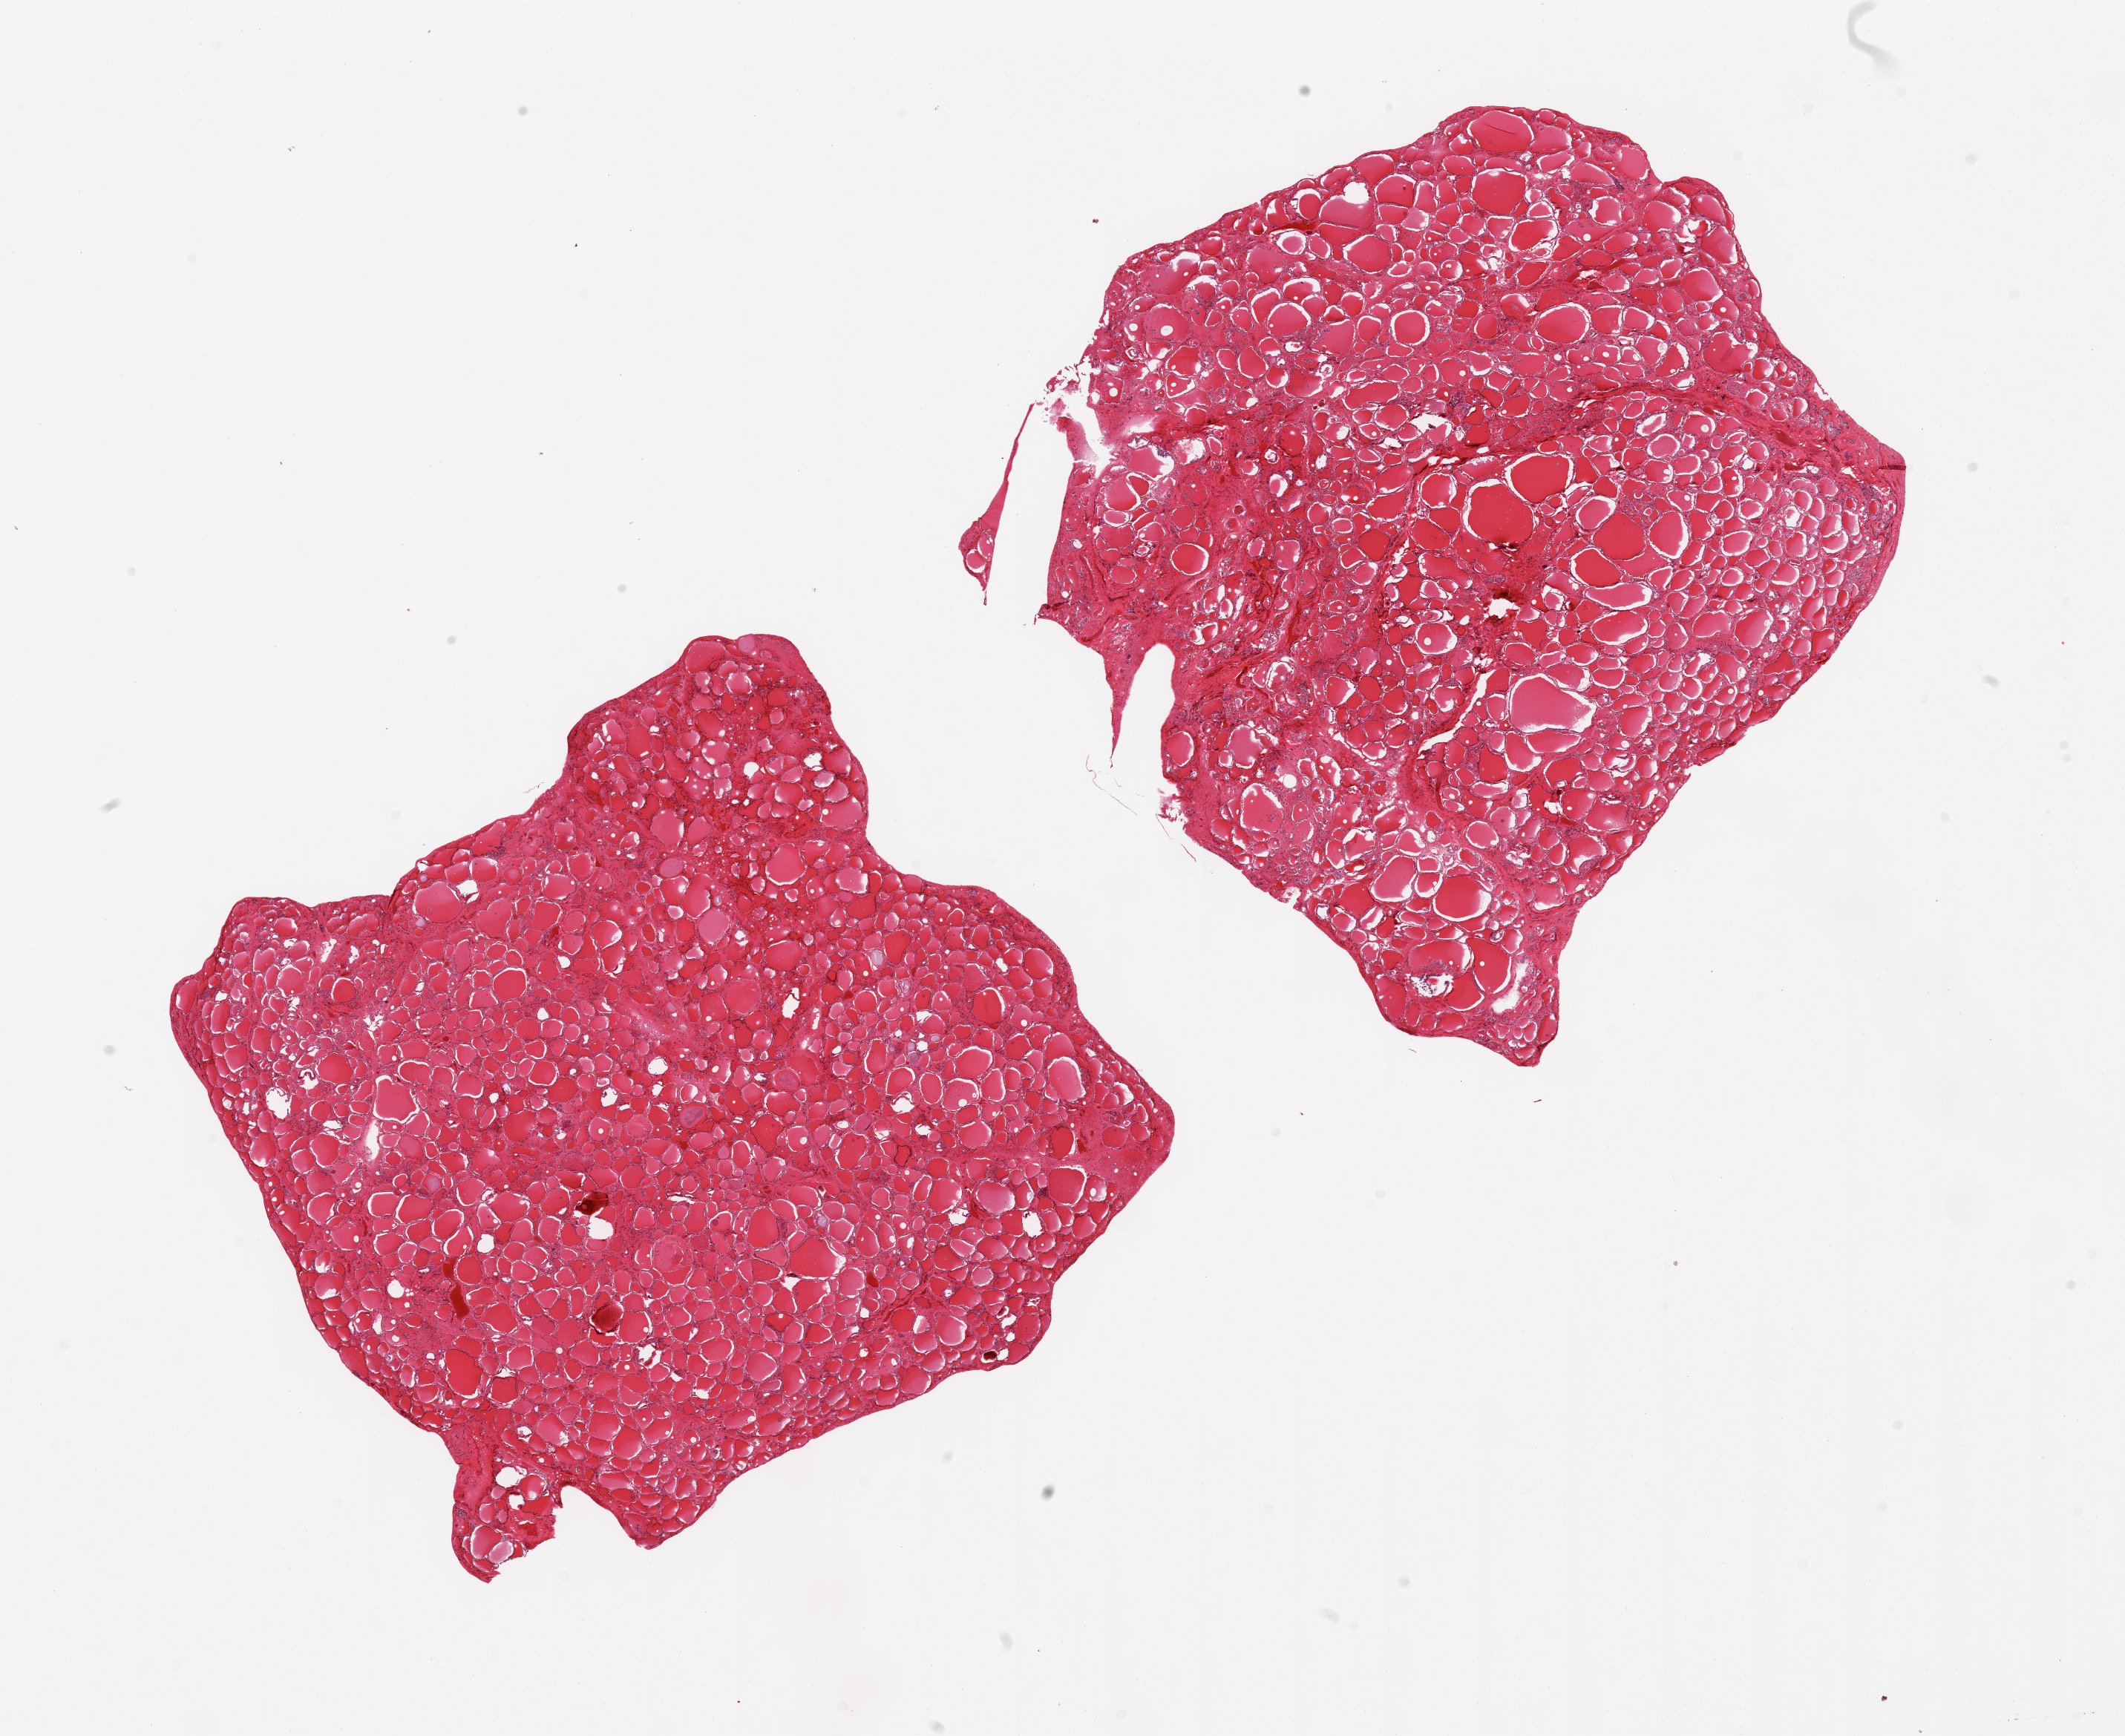
Digitized haematoxylin and eosin-stained section, brightfield, a low-resolution overview of the entire scanned area, about 22.6 x 18.5 mm (from a 20x scan); PAXgene-fixed, paraffin-embedded tissue; target tissue: thyroid; donor tissue sample.
Reviewer comment on this tissue sample: 2 pieces.